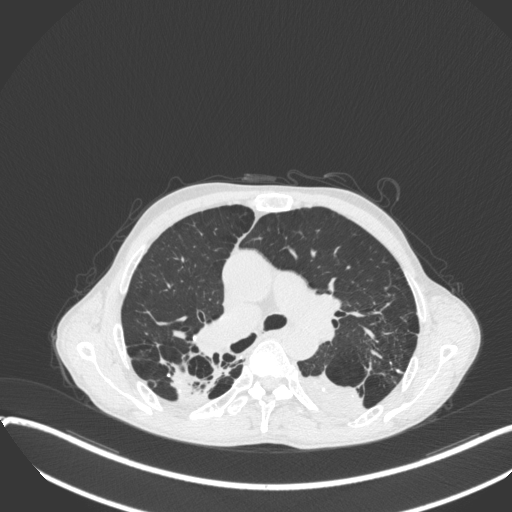
Chest CT, one axial slice. Slice 243 of 400 in the series (ordered by position). Reconstruction kernel B31f. 120 kVp. Lung window (W 1500 / L -600 HU). 1 mm slice thickness. 512 × 512 image matrix, field of view 400 × 400 mm. Patient: male, 57 years. Case-level facts recorded for this patient, not image findings: clinical TNM (as recorded): T4 N0 M0.
Structures marked on this image (rectangle marked by the reading radiologist):
- lung tumour (recorded histology: squamous cell carcinoma): box from (x=295, y=366) to (x=366, y=422) px